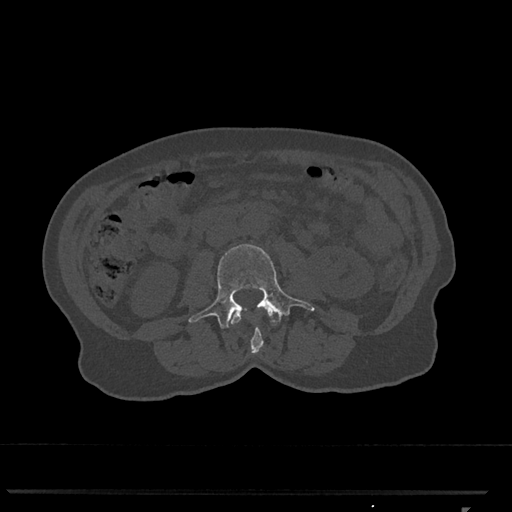
CT including the spine, one axial slice; position 287 of 793 along the scan axis; reconstruction kernel Br40s/3; 120 kVp; bone window (W 1800 / L 400 HU); 512 × 512 image matrix, field of view 380 × 380 mm. Patient: female, 62 years. From the clinical record (not read from this slice): primary cancer: renal.
Structures marked on this image (semi-automatically segmented with operator editing):
- L2 vertebra: bounding box (x1, y1, x2, y2) in pixels: (230, 308, 279, 354)
- L3 vertebra: (188, 244, 315, 329)